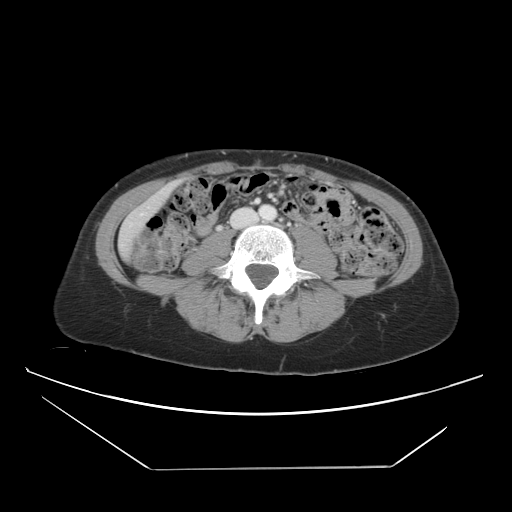
Contrast-enhanced abdominal CT, one axial slice. Position 7 of 42 along the scan axis. Intravenous contrast given. Soft-tissue window (W 400 / L 40 HU). 5 mm slice thickness. 512 × 512 image matrix, field of view 399 × 399 mm. Female patient, age 52 years. From the clinical record (not read from this slice): diagnosis: colorectal cancer liver metastases, imaged before liver resection; multiple liver metastases: yes; largest metastasis: 5.5 cm; chemotherapy before resection: yes.
Outlined on this slice (manually delineated by an expert):
- hepatic veins: bounding box (x1, y1, x2, y2) in pixels: (130, 206, 149, 226)
- liver: (122, 187, 171, 255)
- planned liver remnant (the part of the liver to remain after resection): (130, 186, 172, 224)
- portal vein (with intrahepatic branches): (255, 199, 259, 204)